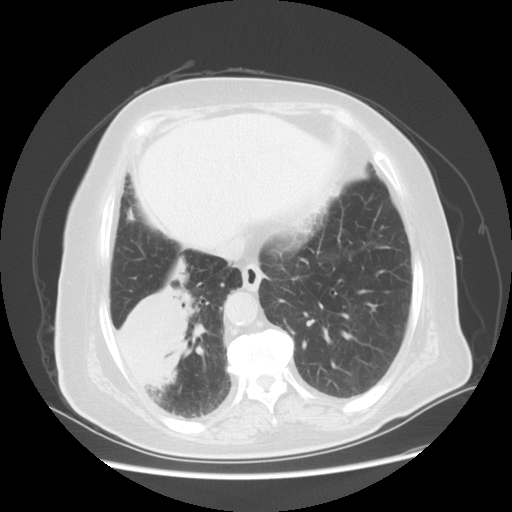
Chest CT, one axial slice; position 17 of 56 along the scan axis; reconstruction kernel STANDARD; 120 kVp; lung window (W 1500 / L -600 HU); 5 mm slice thickness; 512 × 512 image matrix, field of view 378 × 378 mm. Patient: female, 73 years. Case-level facts recorded for this patient, not image findings: clinical TNM (as recorded): T3 N0 M0.
Structures marked on this image (rectangle marked by the reading radiologist):
- lung tumour (recorded histology: adenocarcinoma): bounding box [x1, y1, x2, y2] px = [109, 273, 191, 393]